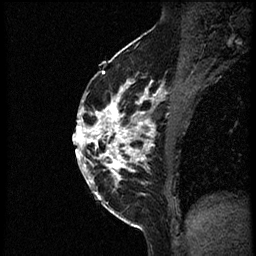
Breast MRI (dynamic contrast-enhanced), one sagittal slice. Position 34 of 56 along the scan axis. Dynamic contrast-enhanced study with each time point stored as its own series, time point 2 of 3 at this slice position (early post-contrast, ordered by acquisition time). 1.5 T. TE 4.2 ms, TR 21.3 ms. 256 × 256 image matrix, field of view 200 × 200 mm. Female patient, age 41 years. Case-level facts recorded for this patient, not image findings: setting: breast cancer imaged before/during neoadjuvant chemotherapy; receptor status: HER2-positive.
Structures marked on this image (semi-automatic segmentation, software-assisted and operator-edited):
- analysis volume of interest (the breast-tissue region the enhancement analysis was run in; not a lesion): bounding box (x1, y1, x2, y2) in pixels: (84, 73, 177, 205)
- tumour enhancement mask (voxels above the 100 % enhancement threshold inside the analysis volume of interest): (84, 79, 163, 197)